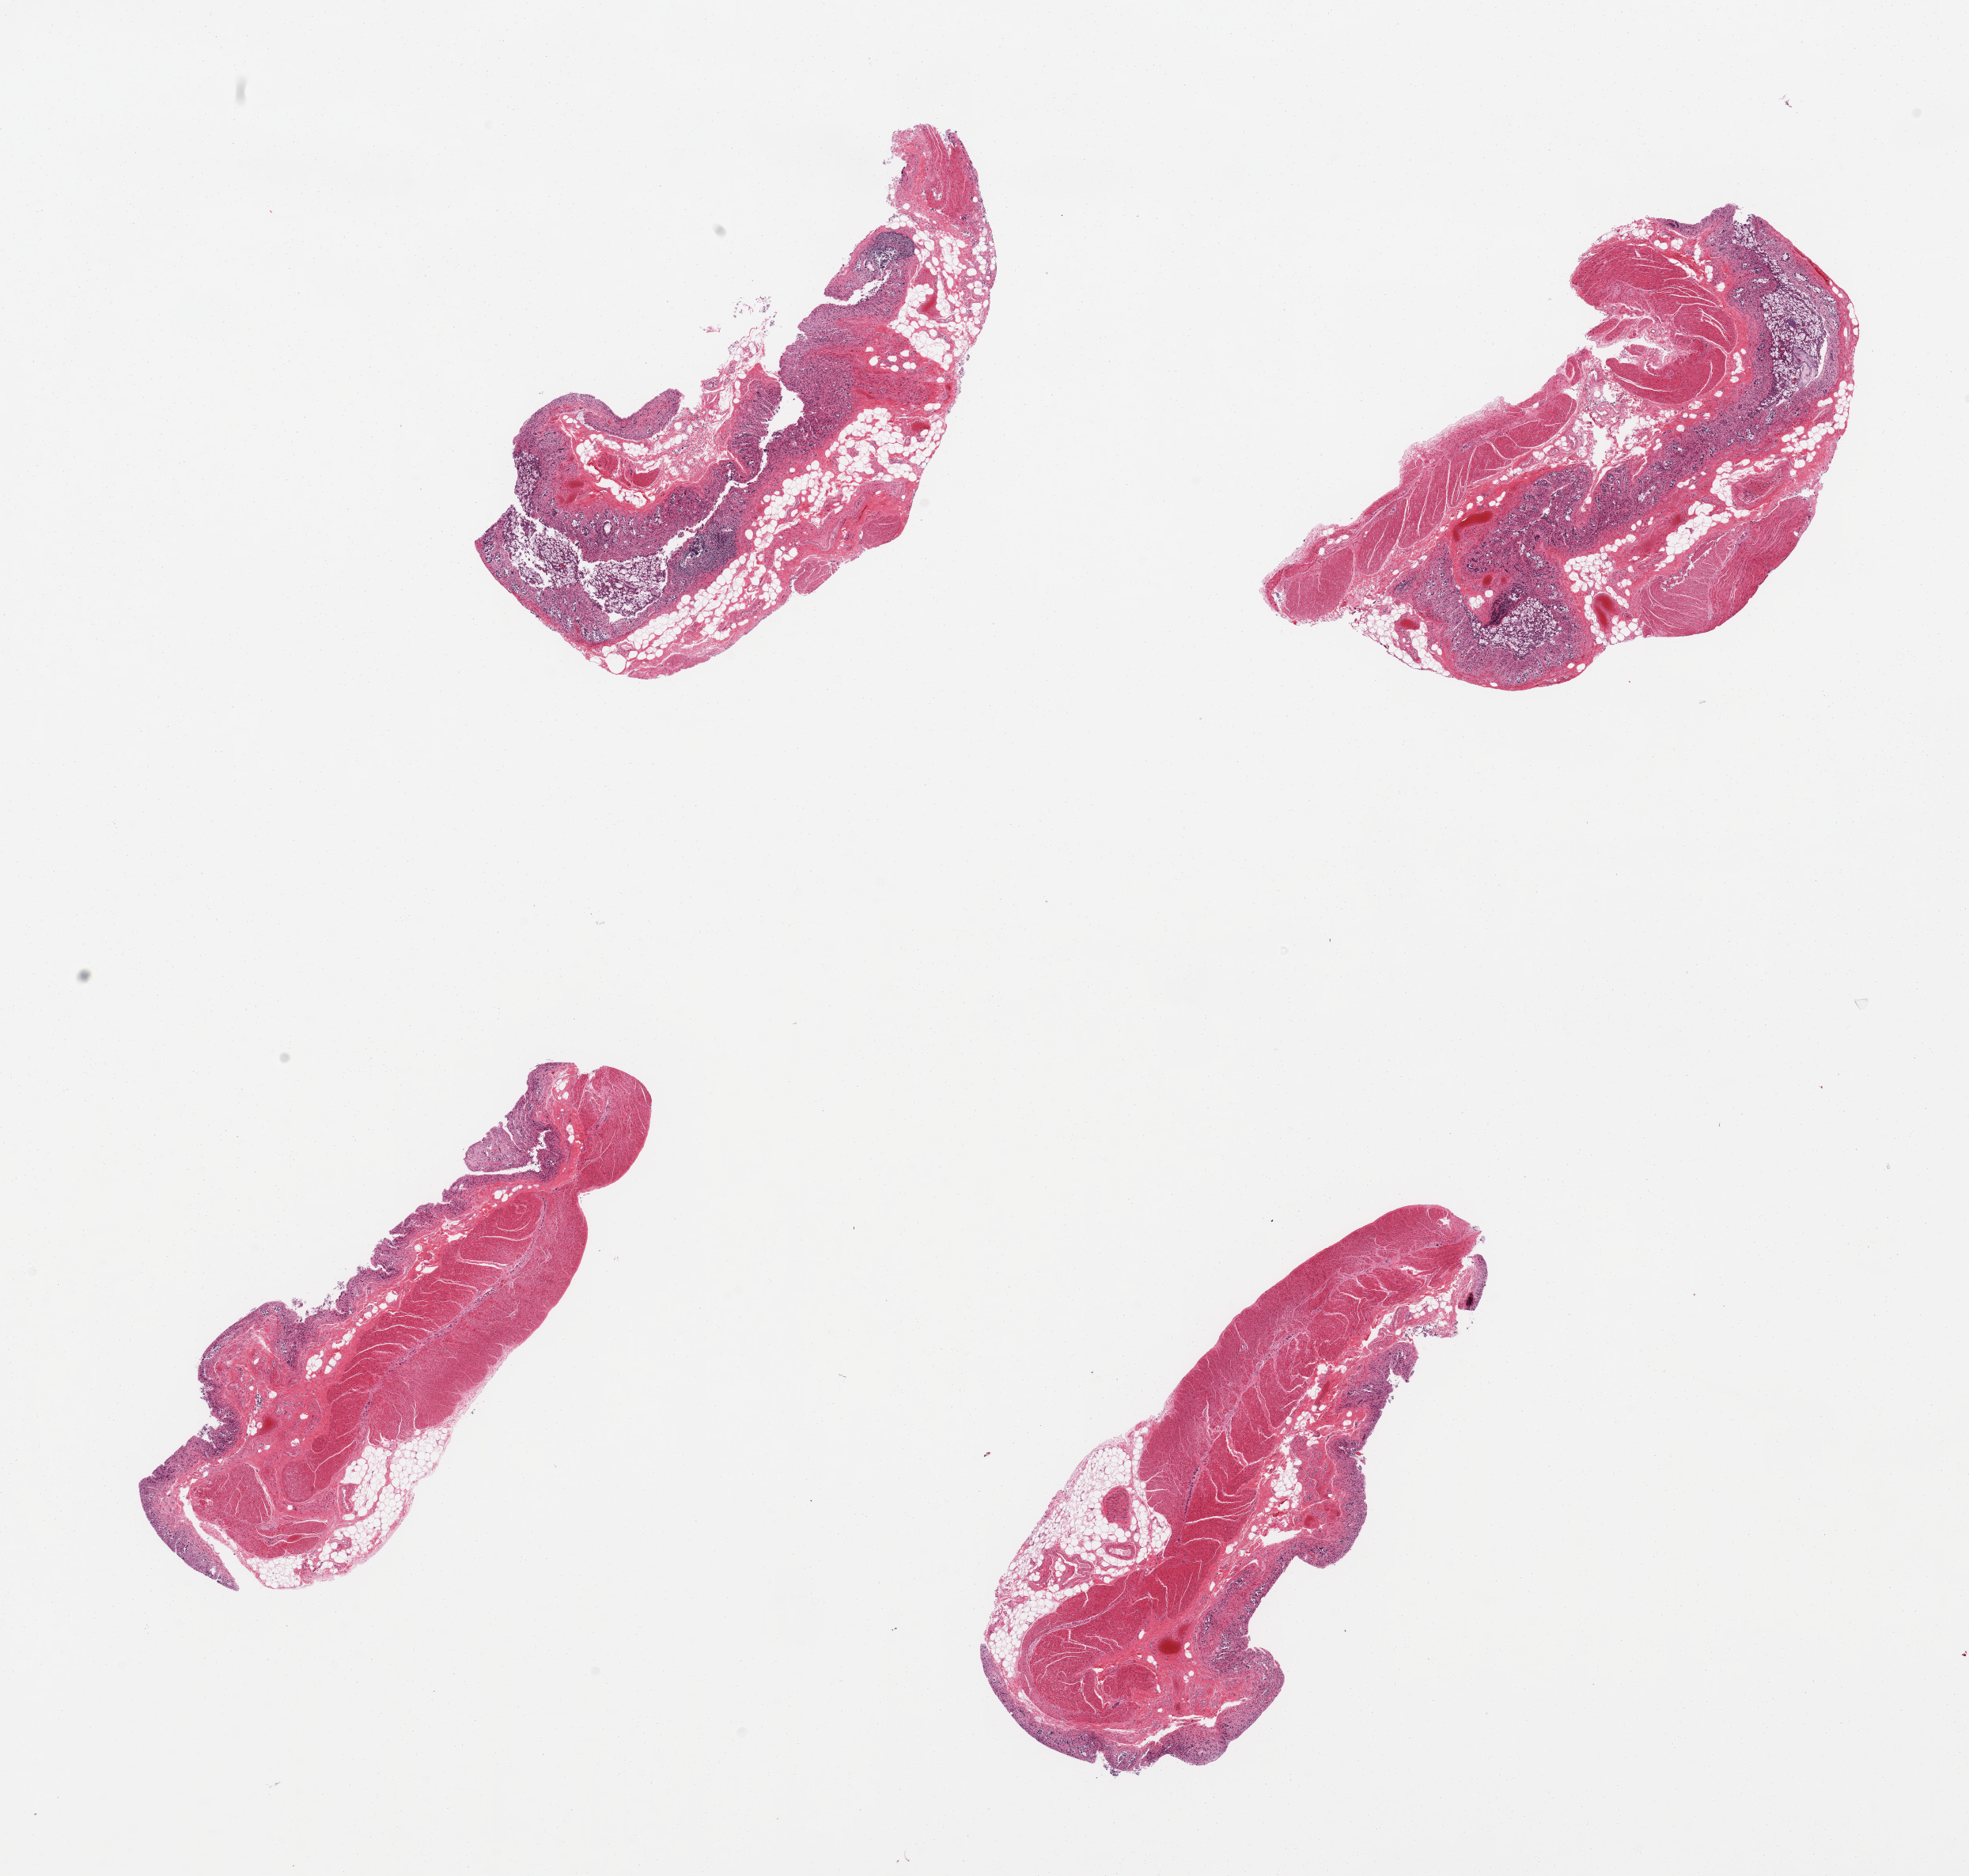
Whole-slide image, hematoxylin and eosin (H&E) stain, shown as a low-resolution overview of the whole scanned area (about 19.7 x 18.8 mm, acquisition: 20x scan); PAXgene-fixed paraffin-embedded (PFPE) section; target tissue: sigmoid colon; donor tissue sample.
Pathologist's review note for this sample: 4 pieces, muscularis (target) and autolyzed mucosa (not target).